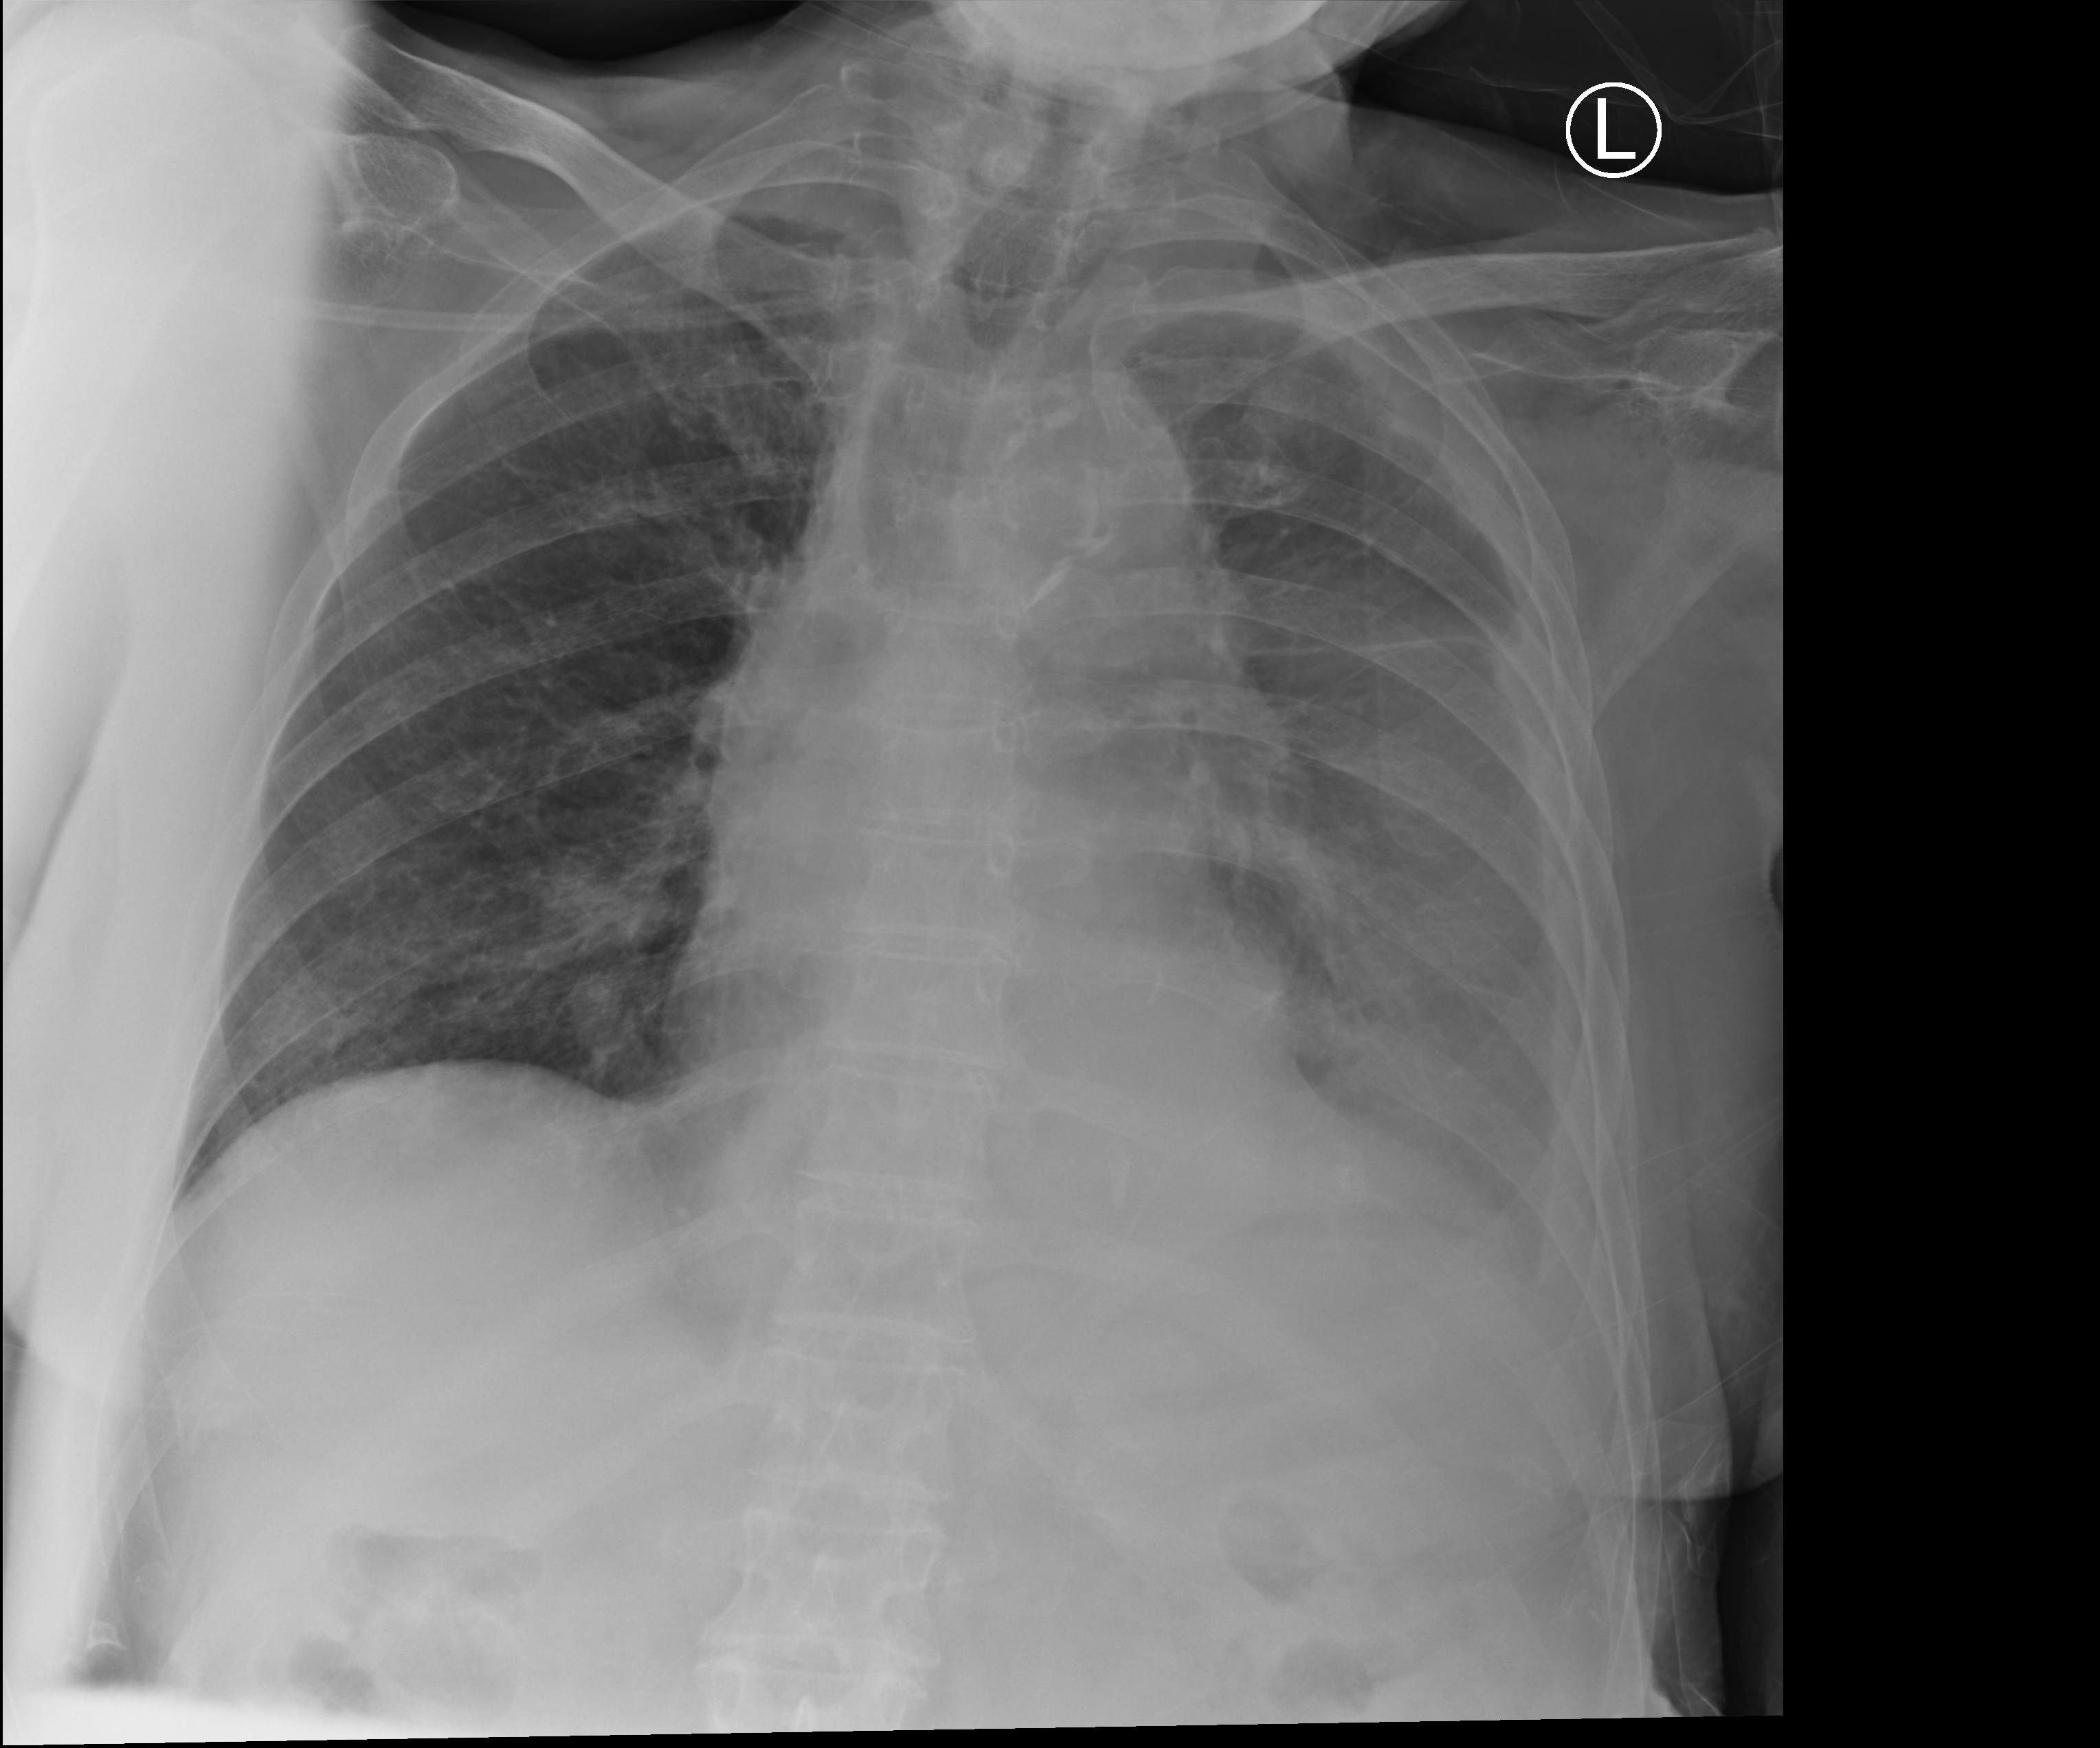
Chest radiograph (computed radiography). Patient hospitalised with COVID-19; female, aged 75–90 years.
Hospital-stay facts (about this admission, not read from this image; timing relative to this image not recorded): length of hospital stay: 8 days; mechanically ventilated during this hospital stay: no; COPD (admission record): no.